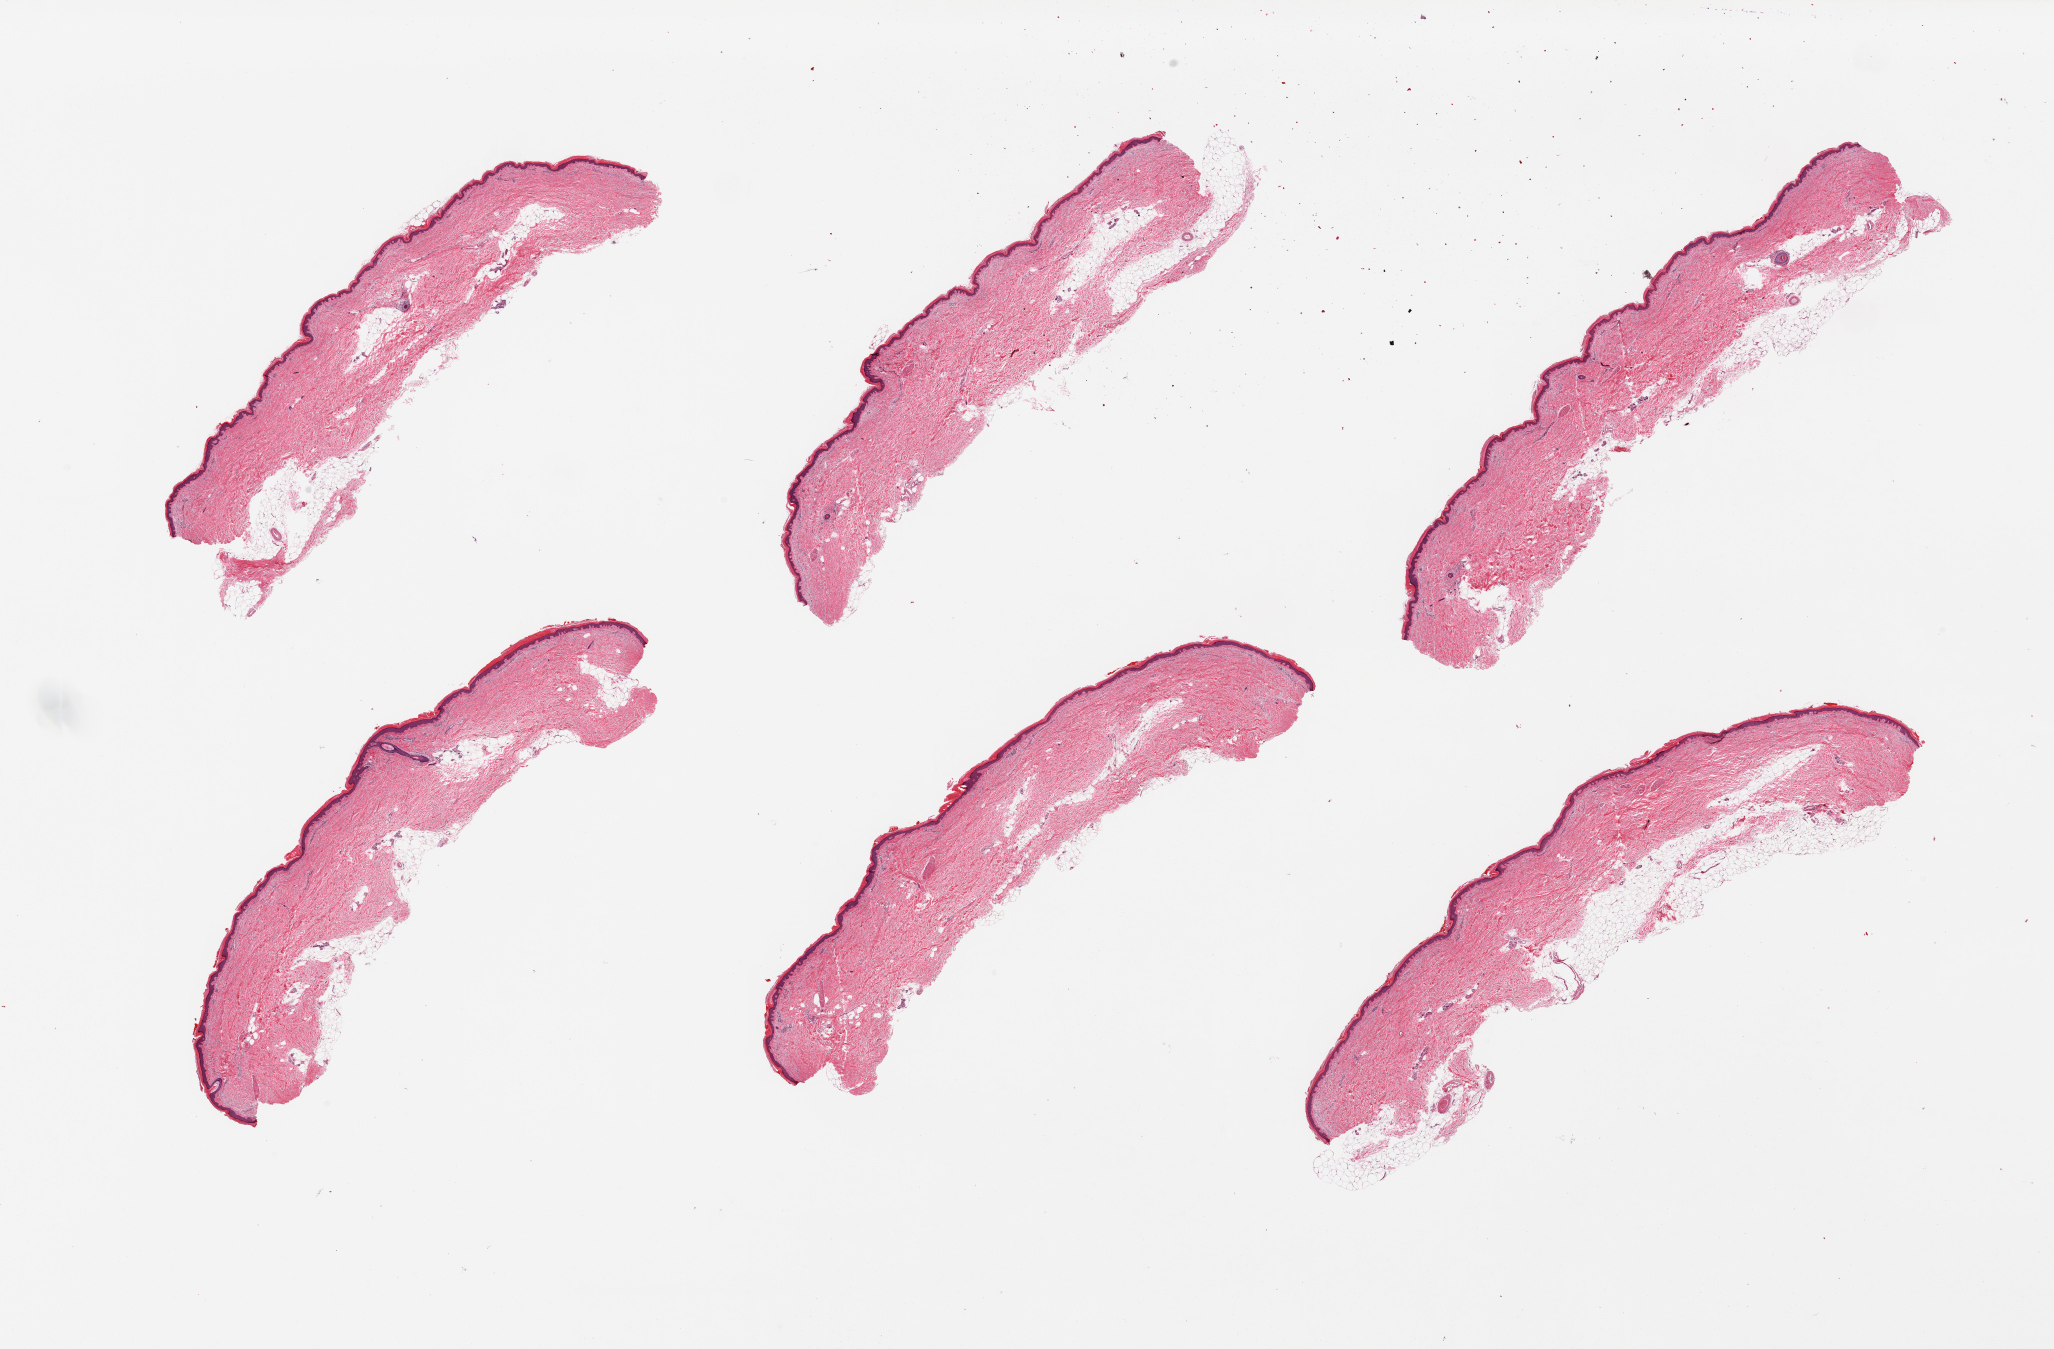
Digitized H&E-stained section, low-resolution overview of the scanned area, about 32.5 x 21.3 mm, PAXgene-fixed, paraffin-embedded tissue, target tissue: skin of lower leg, donor tissue sample. Donor sex: female.
Reviewer comment on this tissue sample: 2 pieces. Well trimmed except for 1mm subcutaneous fat on 1 piece.